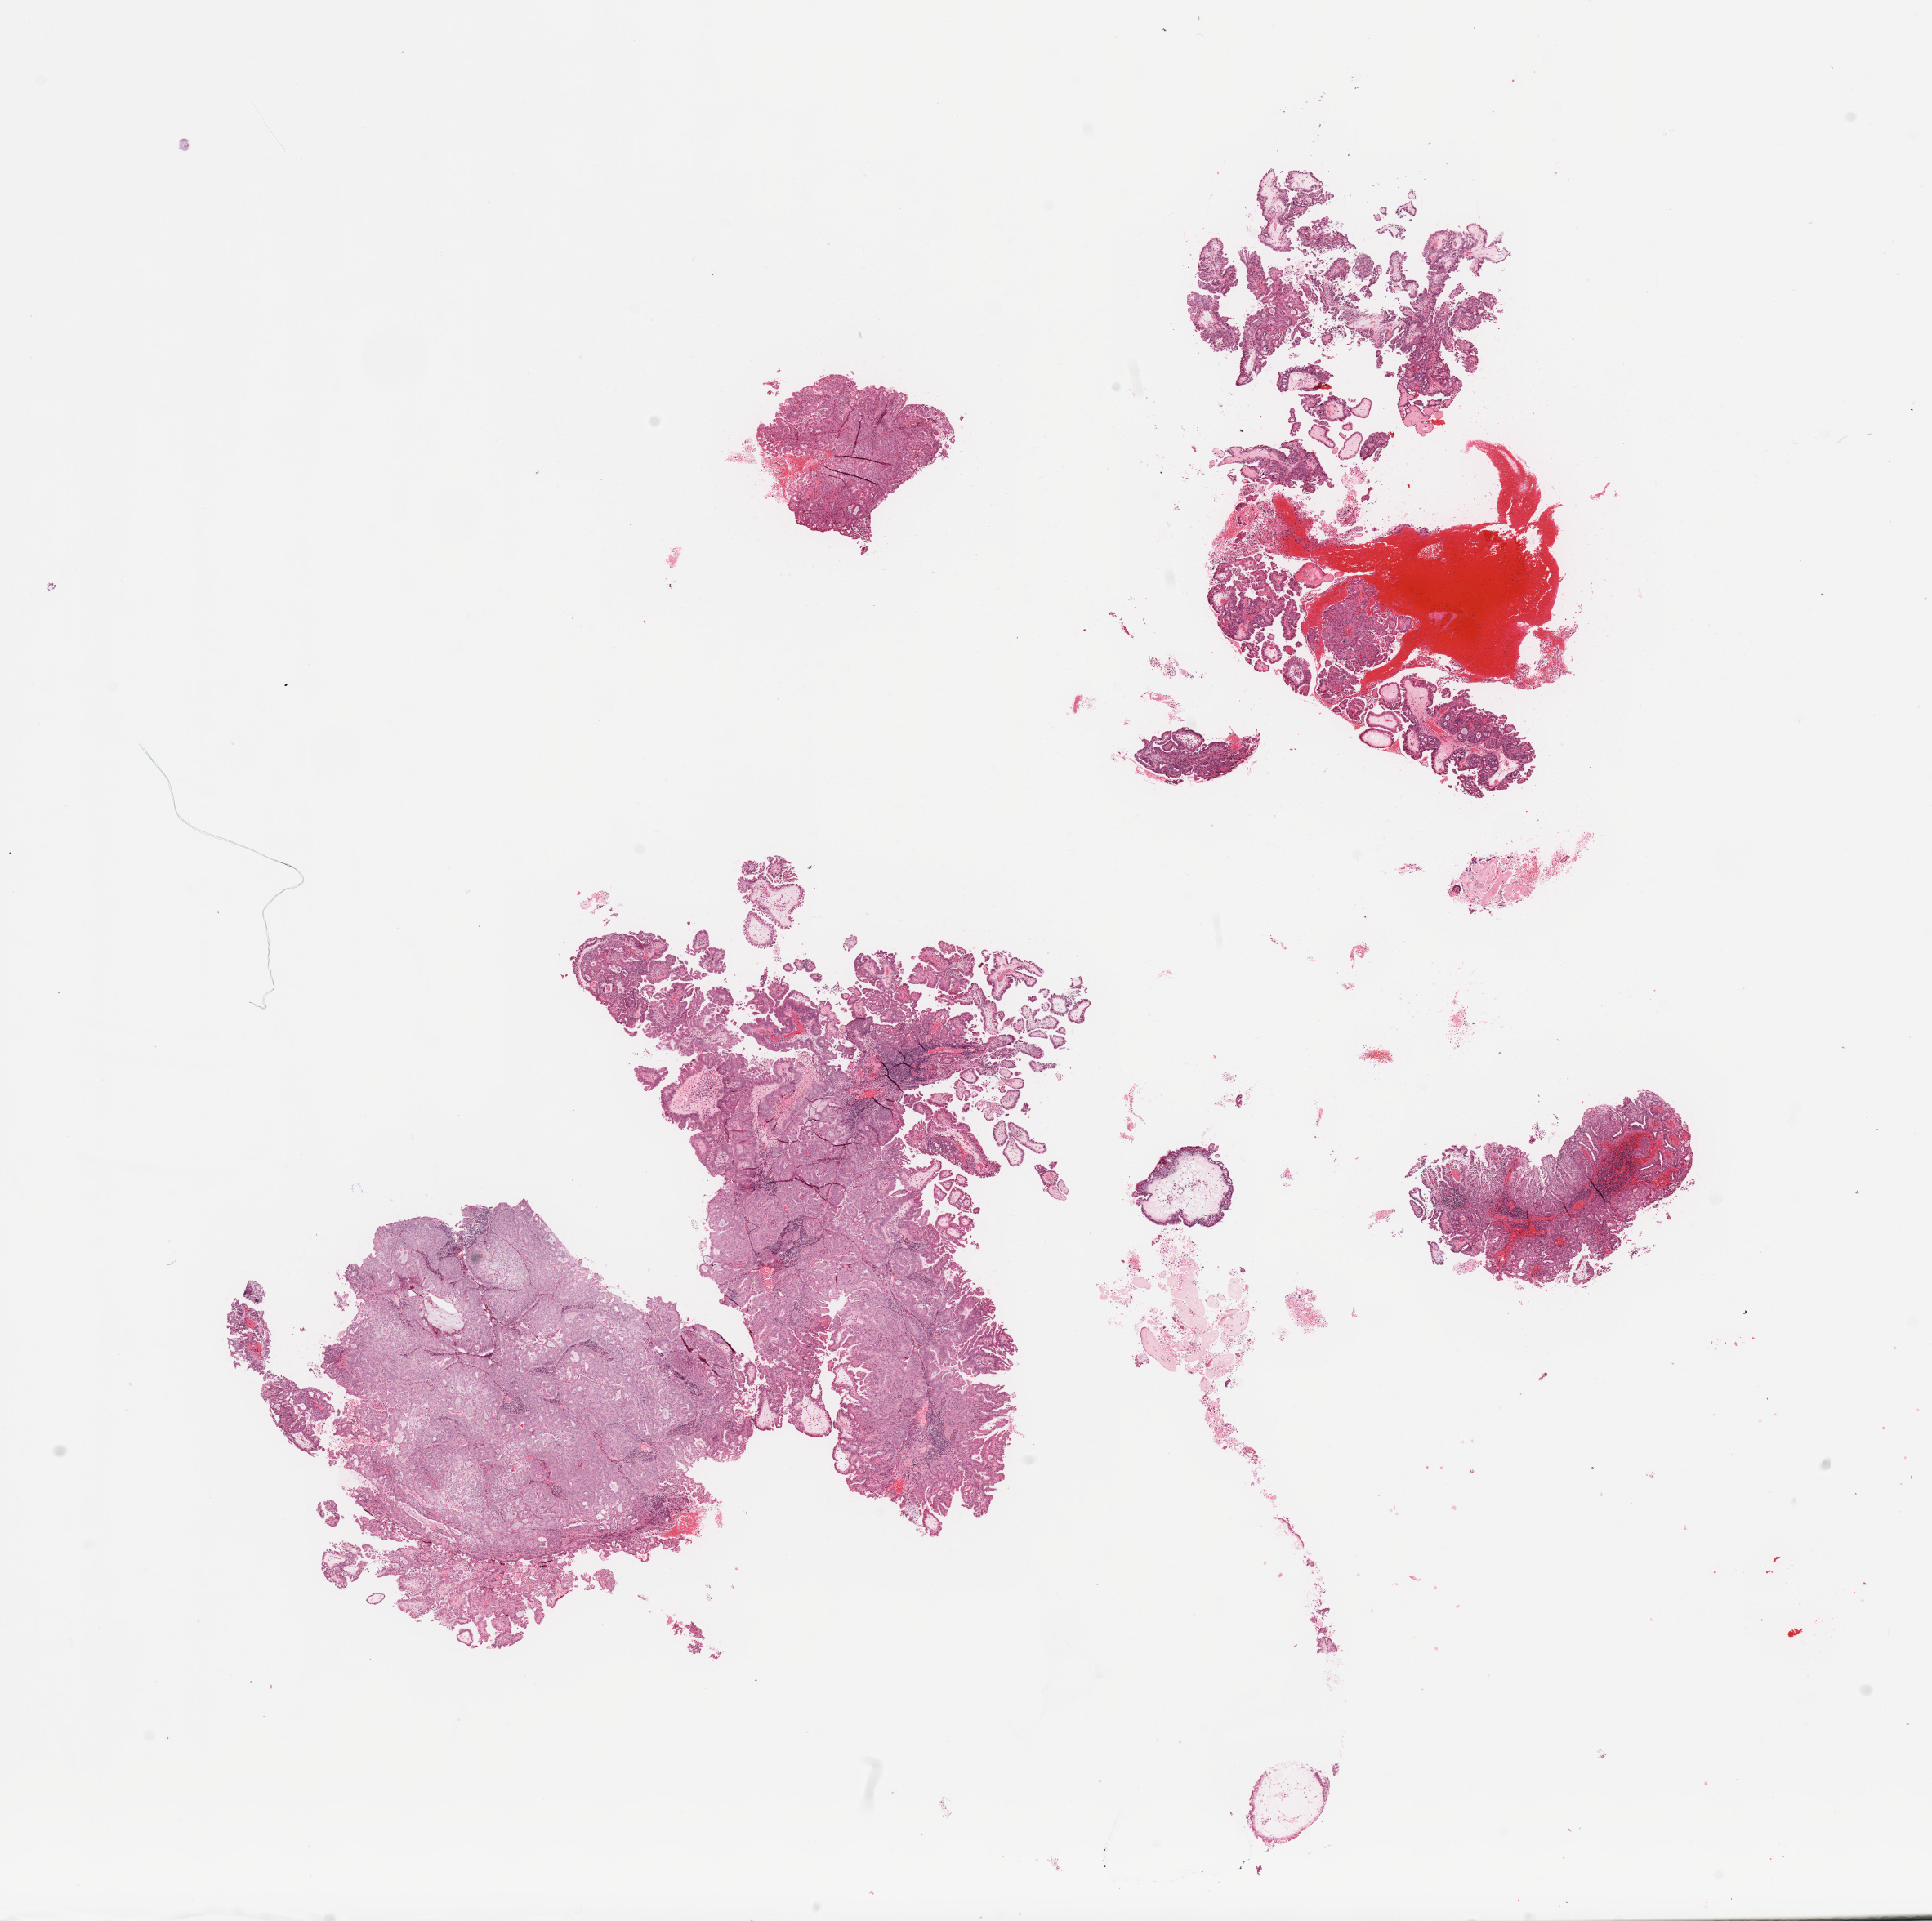
Digitized H&E tissue section (whole slide) — a low-resolution overview of the entire scanned area, about 18.7 x 18.6 mm. Uterus, tumour tissue. Female, 66 y/o.
Diagnosis: Endometrioid adenocarcinoma, NOS.